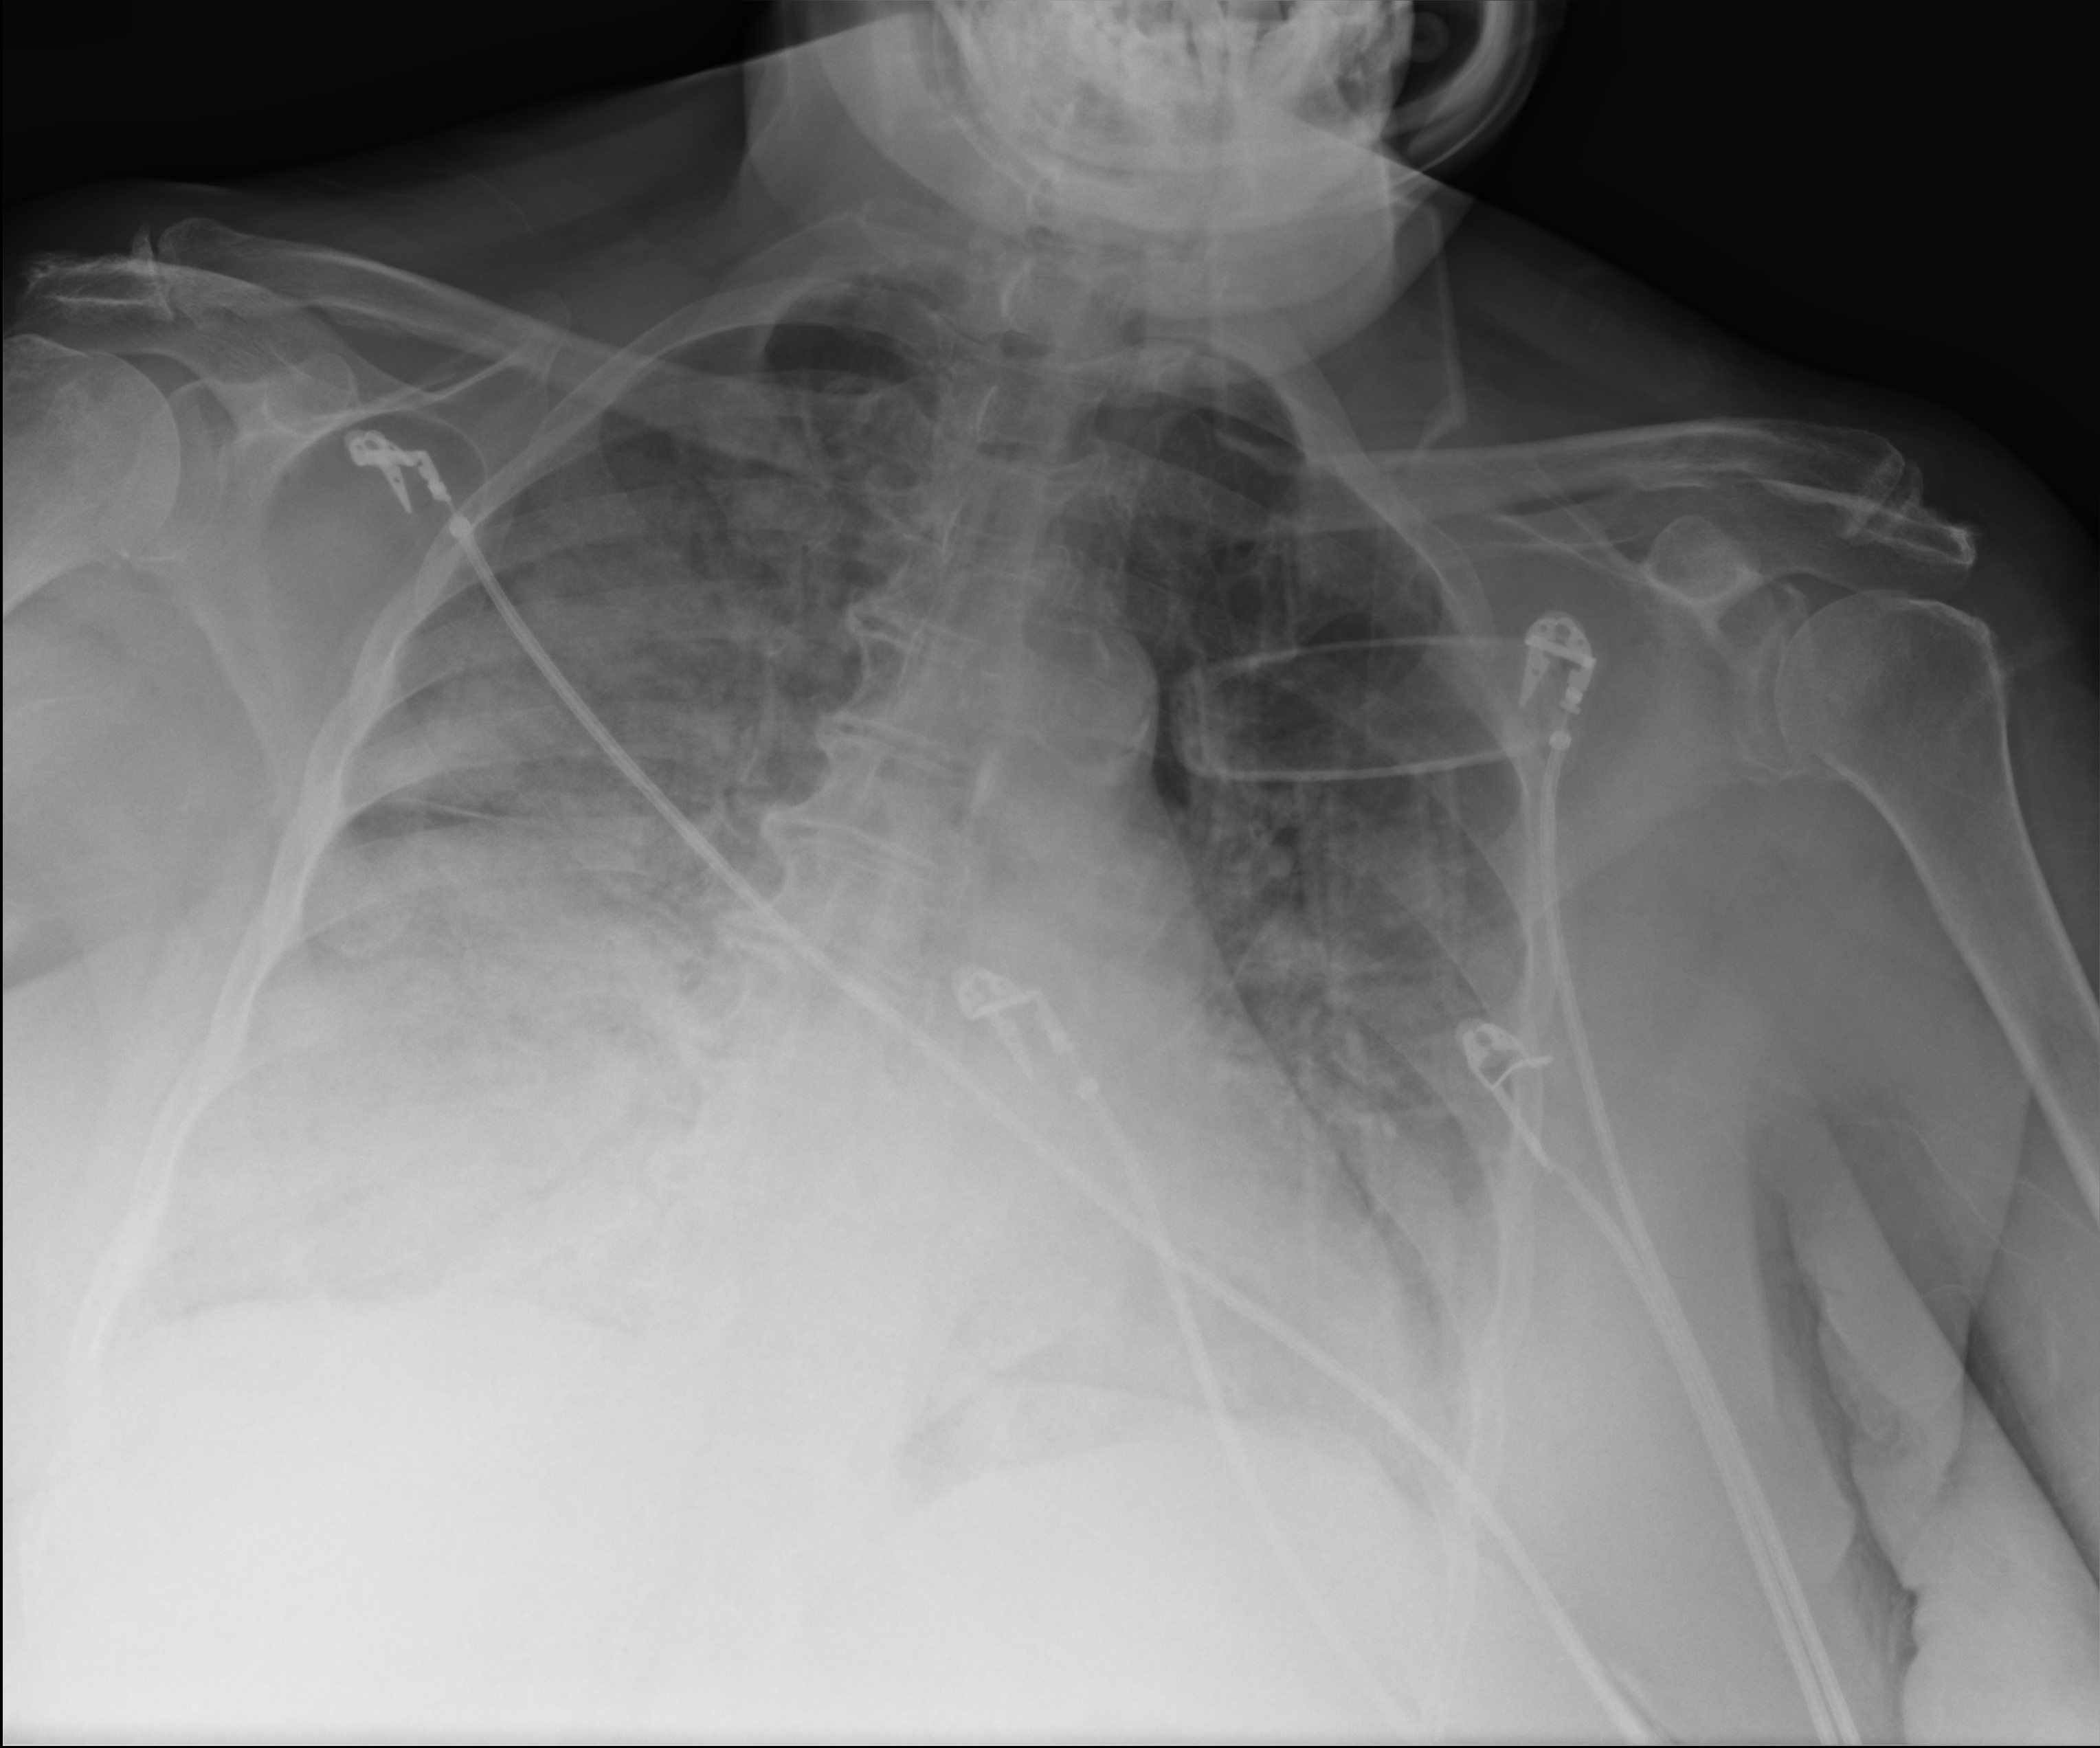
Chest X-ray (portable), anteroposterior (AP) projection. Female patient hospitalised with COVID-19, age 75–90 years.
Admission-level facts for this patient (not findings on this image; timing relative to this image not recorded):
- other chronic lung disease (admission record): no
- admitted to intensive care during this hospital stay: no
- chronic kidney disease (admission record): no